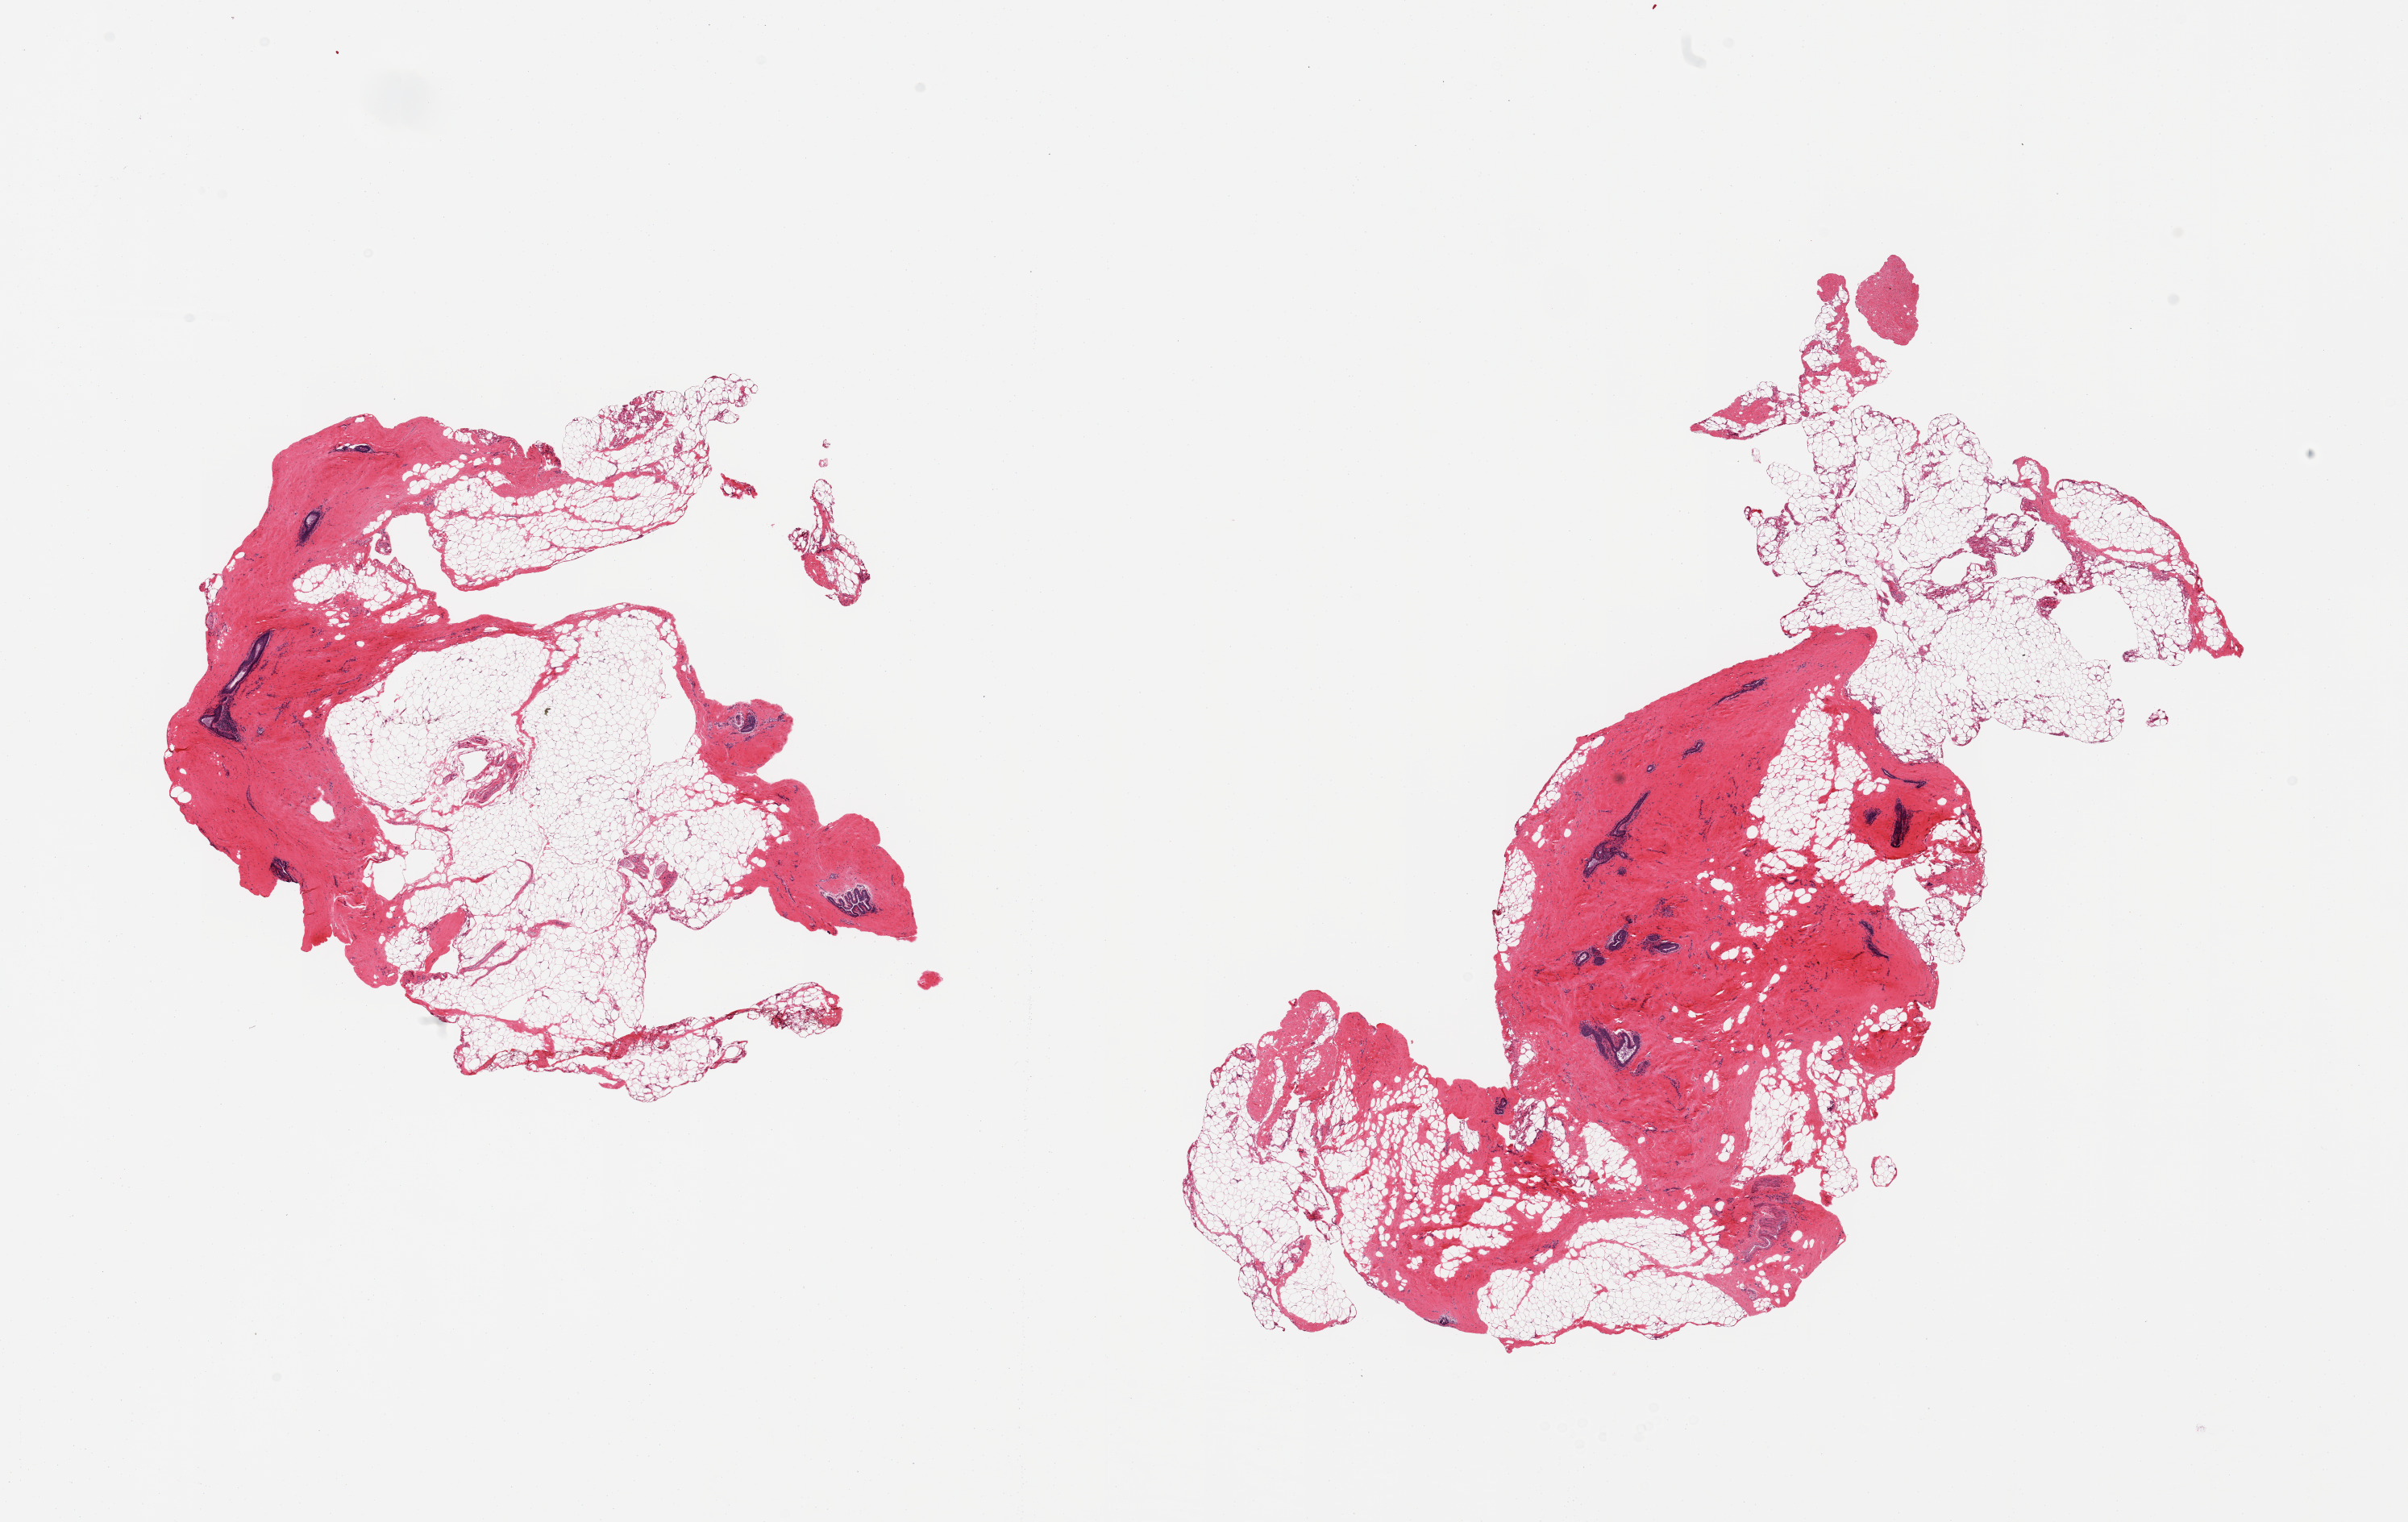
Digitized H&E-stained section — a low-resolution overview of the entire scanned area, about 23.6 x 14.9 mm; PAXgene-fixed paraffin-embedded (PFPE) section; section of breast (target tissue); donor tissue sample. Donor: male.
Pathologist's review note for this sample: 2 pieces; fibroadipose tissue and mammary ducts with periductal lymphocytic infiltrate and stromal fibrosis/hyalinization.